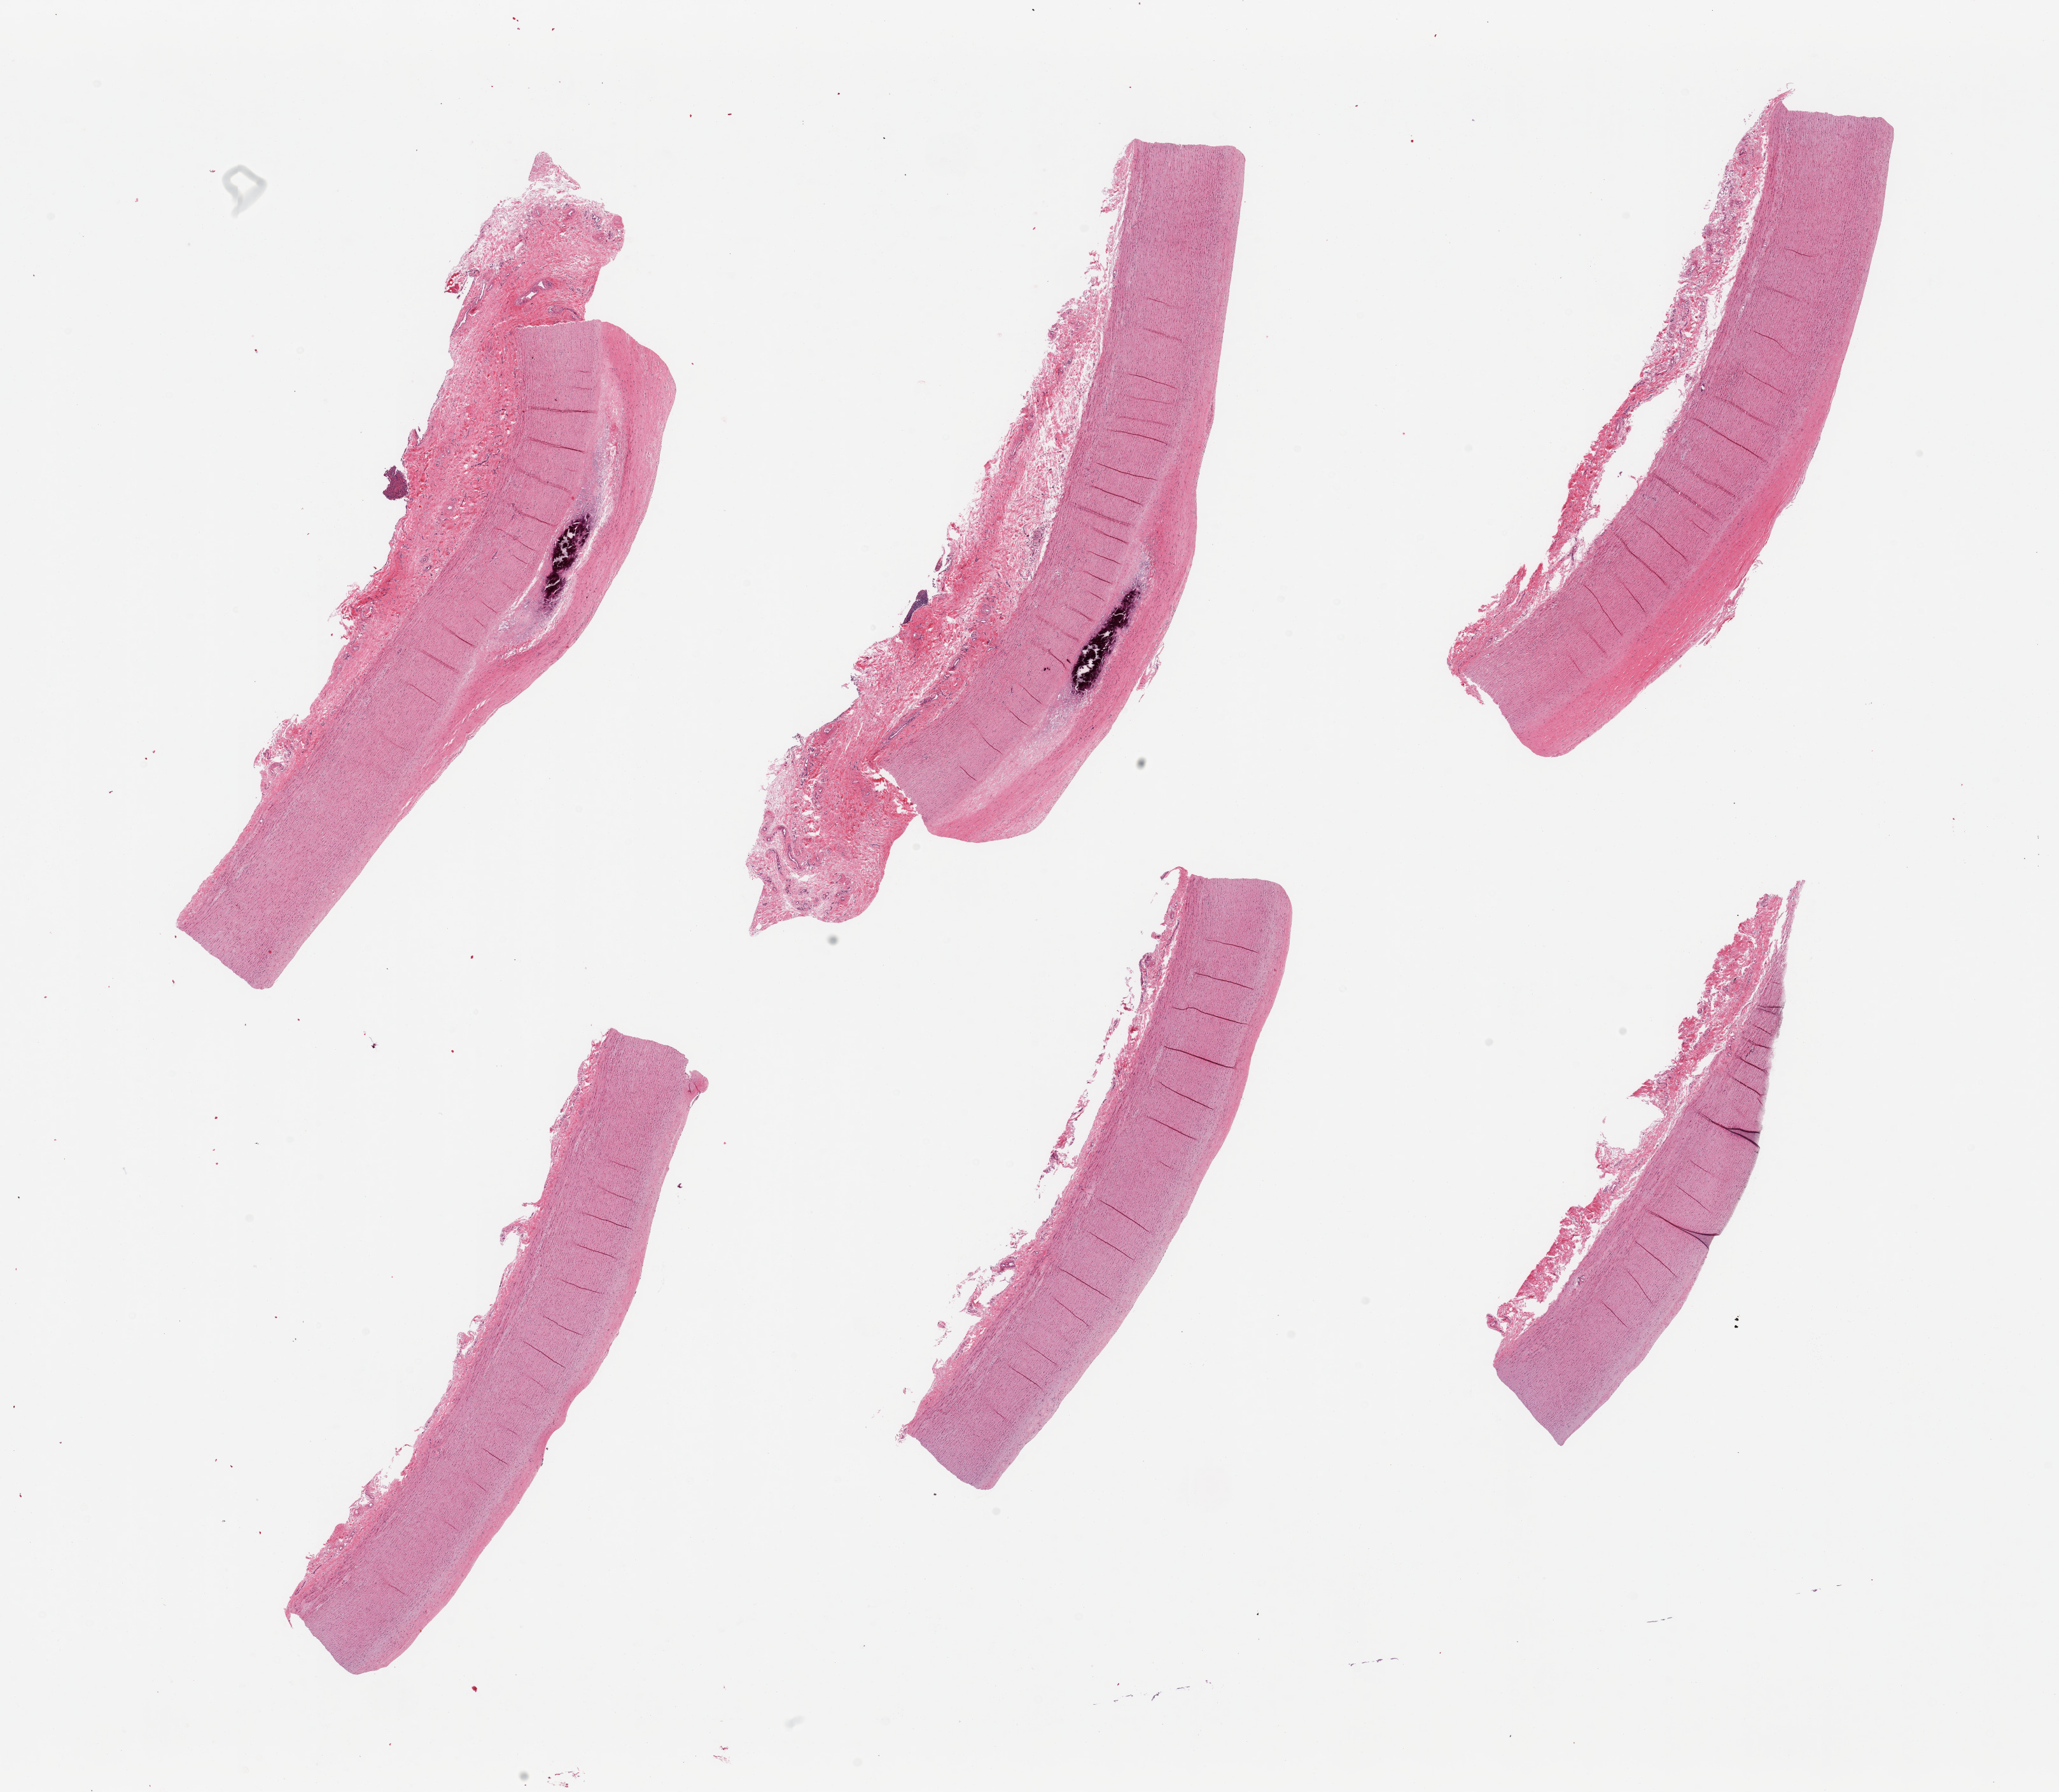
Digitized hematoxylin and eosin (H&E)-stained section, low-resolution overview of the scanned area, about 25.6 x 22.3 mm (acquisition: 20x scan); PAXgene-fixed paraffin-embedded (PFPE) section; sampled site (target tissue): aorta; donor tissue sample. Donor sex: male.
Pathologist's review note for this sample: 6 pieces; moderate atheromatous plaque; focal calcification in 2 pieces.